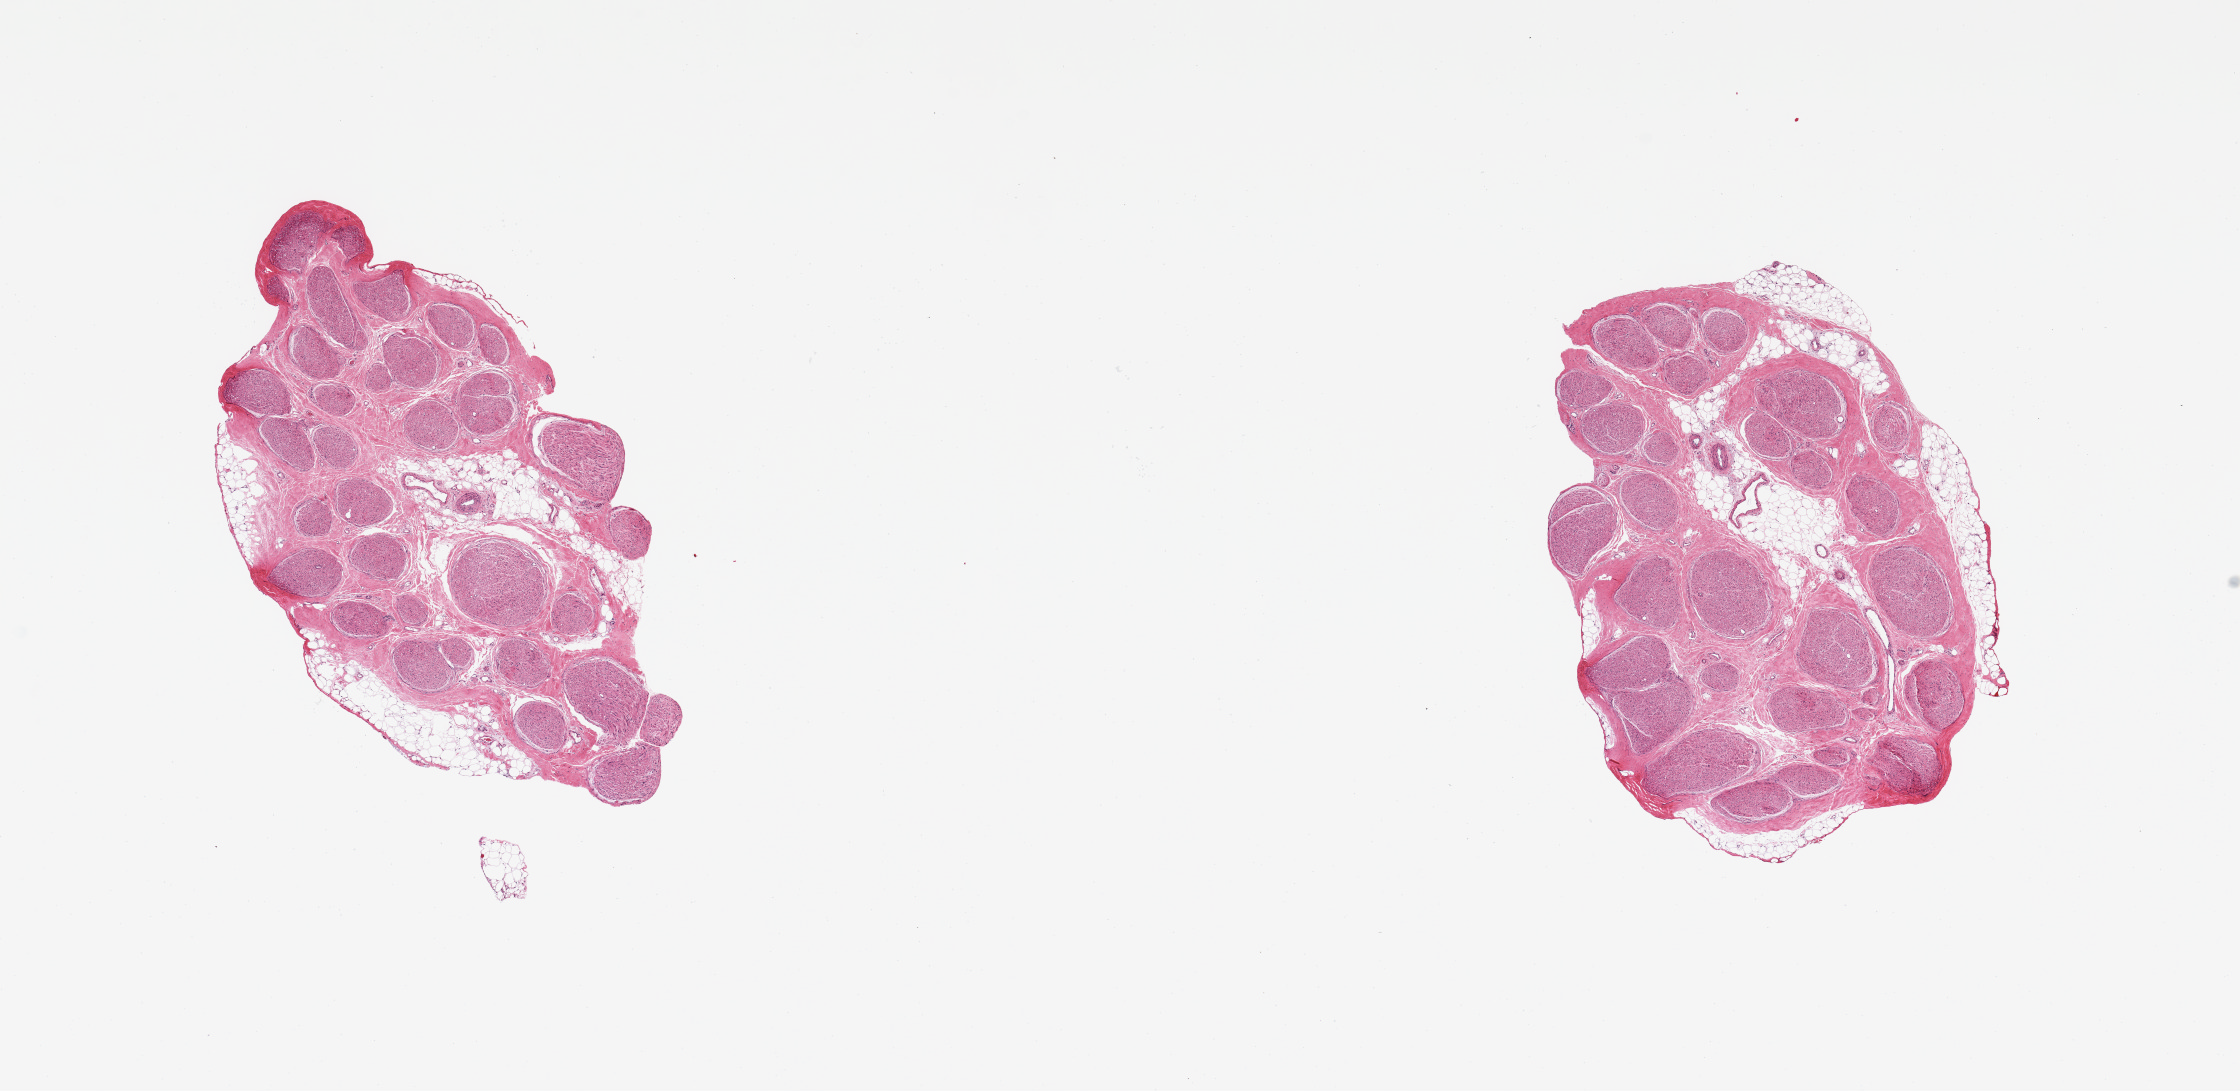
Whole-slide image, hematoxylin and eosin (H&E) stain, whole scanned area (about 17.7 x 8.6 mm, from a 20x scan) shown as a low-resolution overview, PAXgene-fixed paraffin-embedded (PFPE) section, target tissue: tibial nerve, donor tissue sample. Donor sex: male.
• review note (as recorded): 2 pieces, trace adherent fat